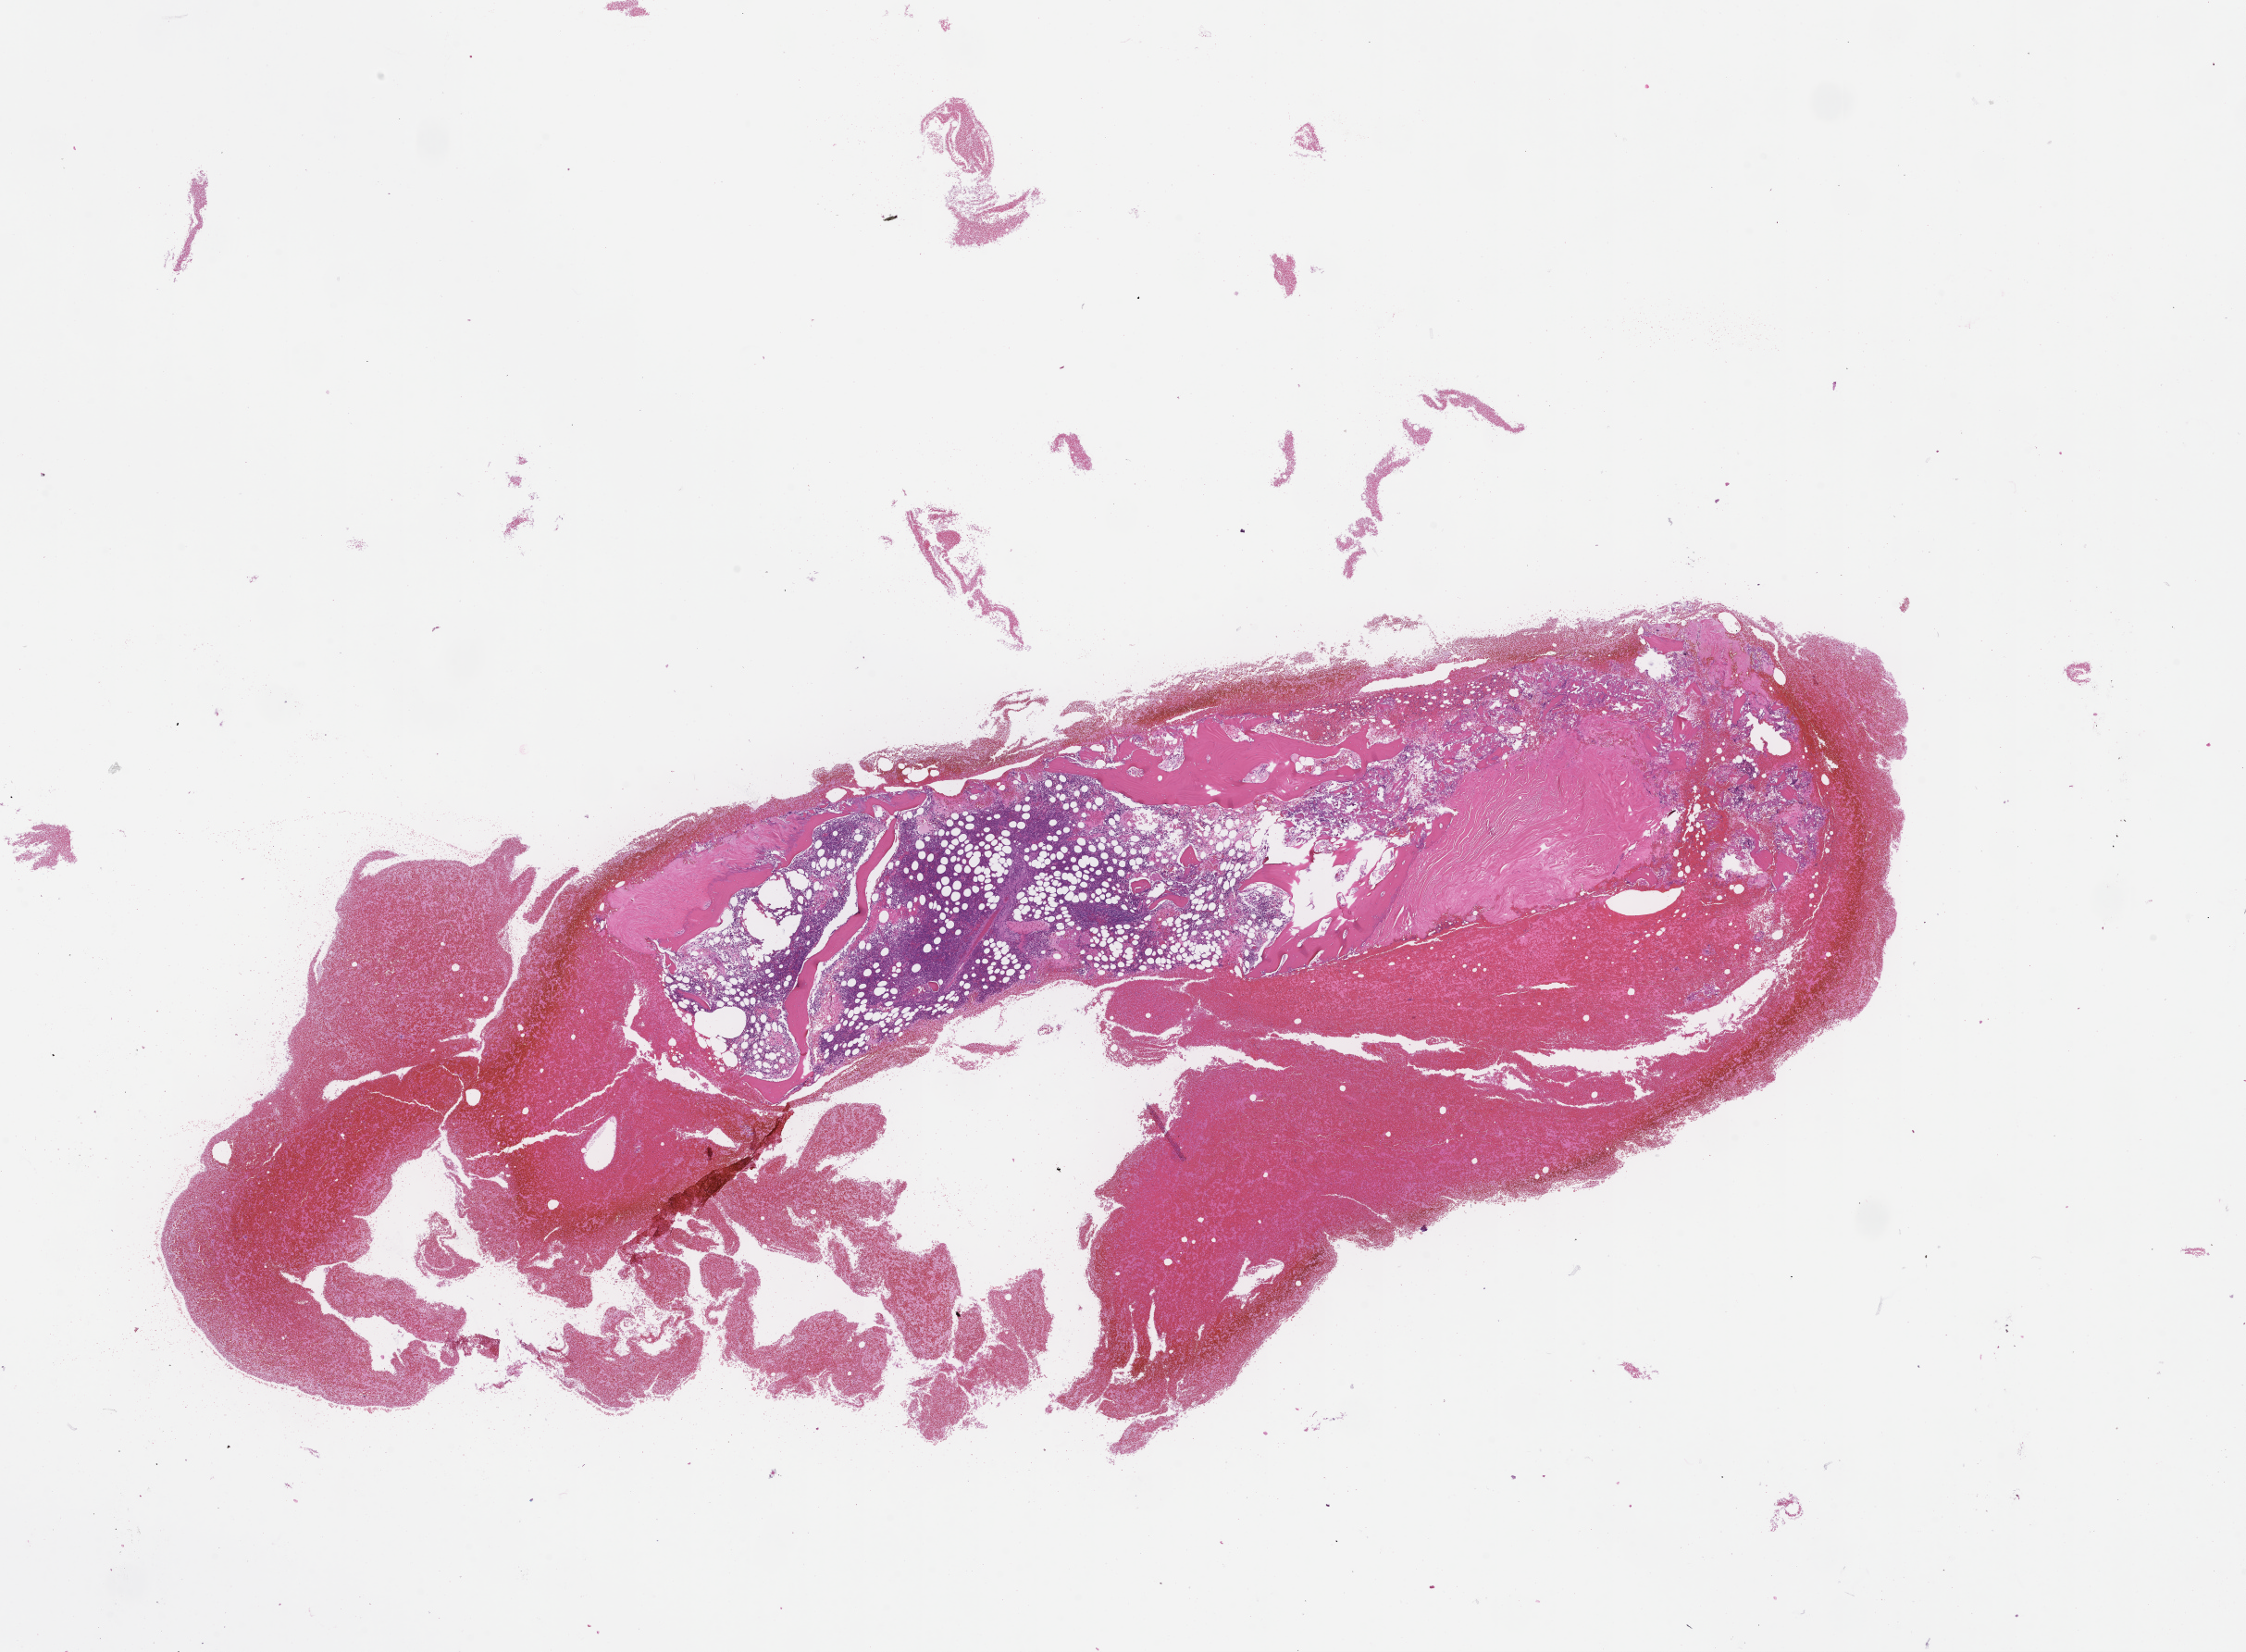
Hematoxylin and eosin (H&E) whole-slide image — whole scanned area (about 19.6 x 14.4 mm) shown as a low-resolution overview; FFPE section; tissue site: bone marrow. Patient sex: male.
- this section: primary tumor
- diagnosis: Plasma Cell Myeloma